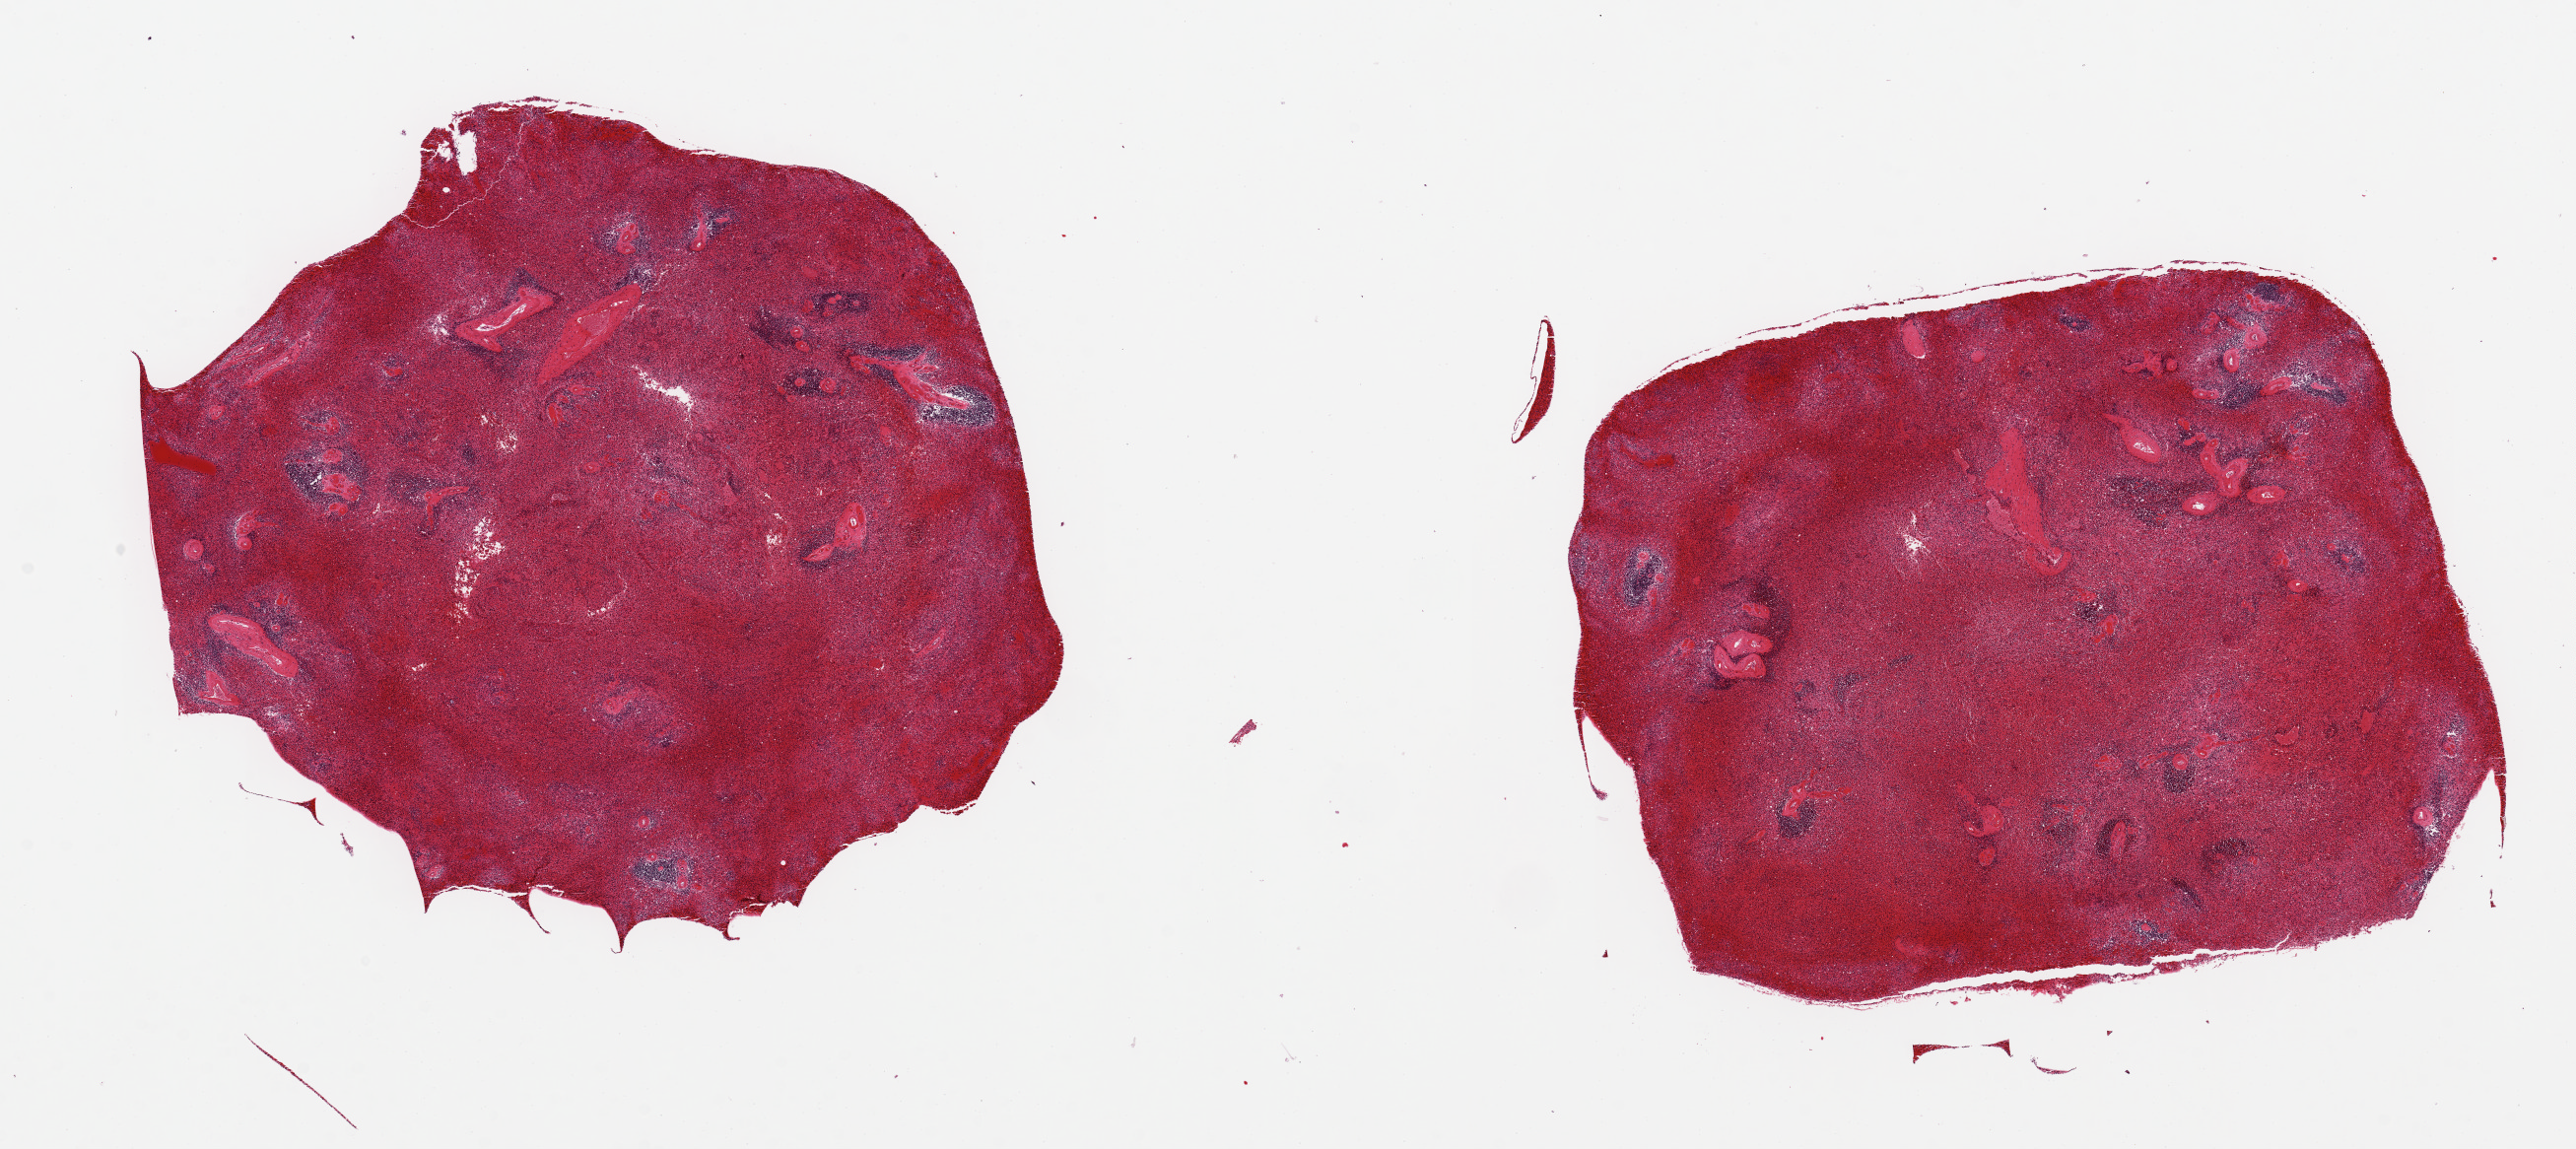
Digitized haematoxylin and eosin-stained section — shown as a low-resolution overview of the whole scanned area (about 20.7 x 9.2 mm). PAXgene-fixed, paraffin-embedded tissue. Sampled site (target tissue): spleen. Tissue donor sample. Donor sex: male.
- review note (as recorded): 2 alliquots, ~6.5x5. Badly autolyzed, congested red pulp